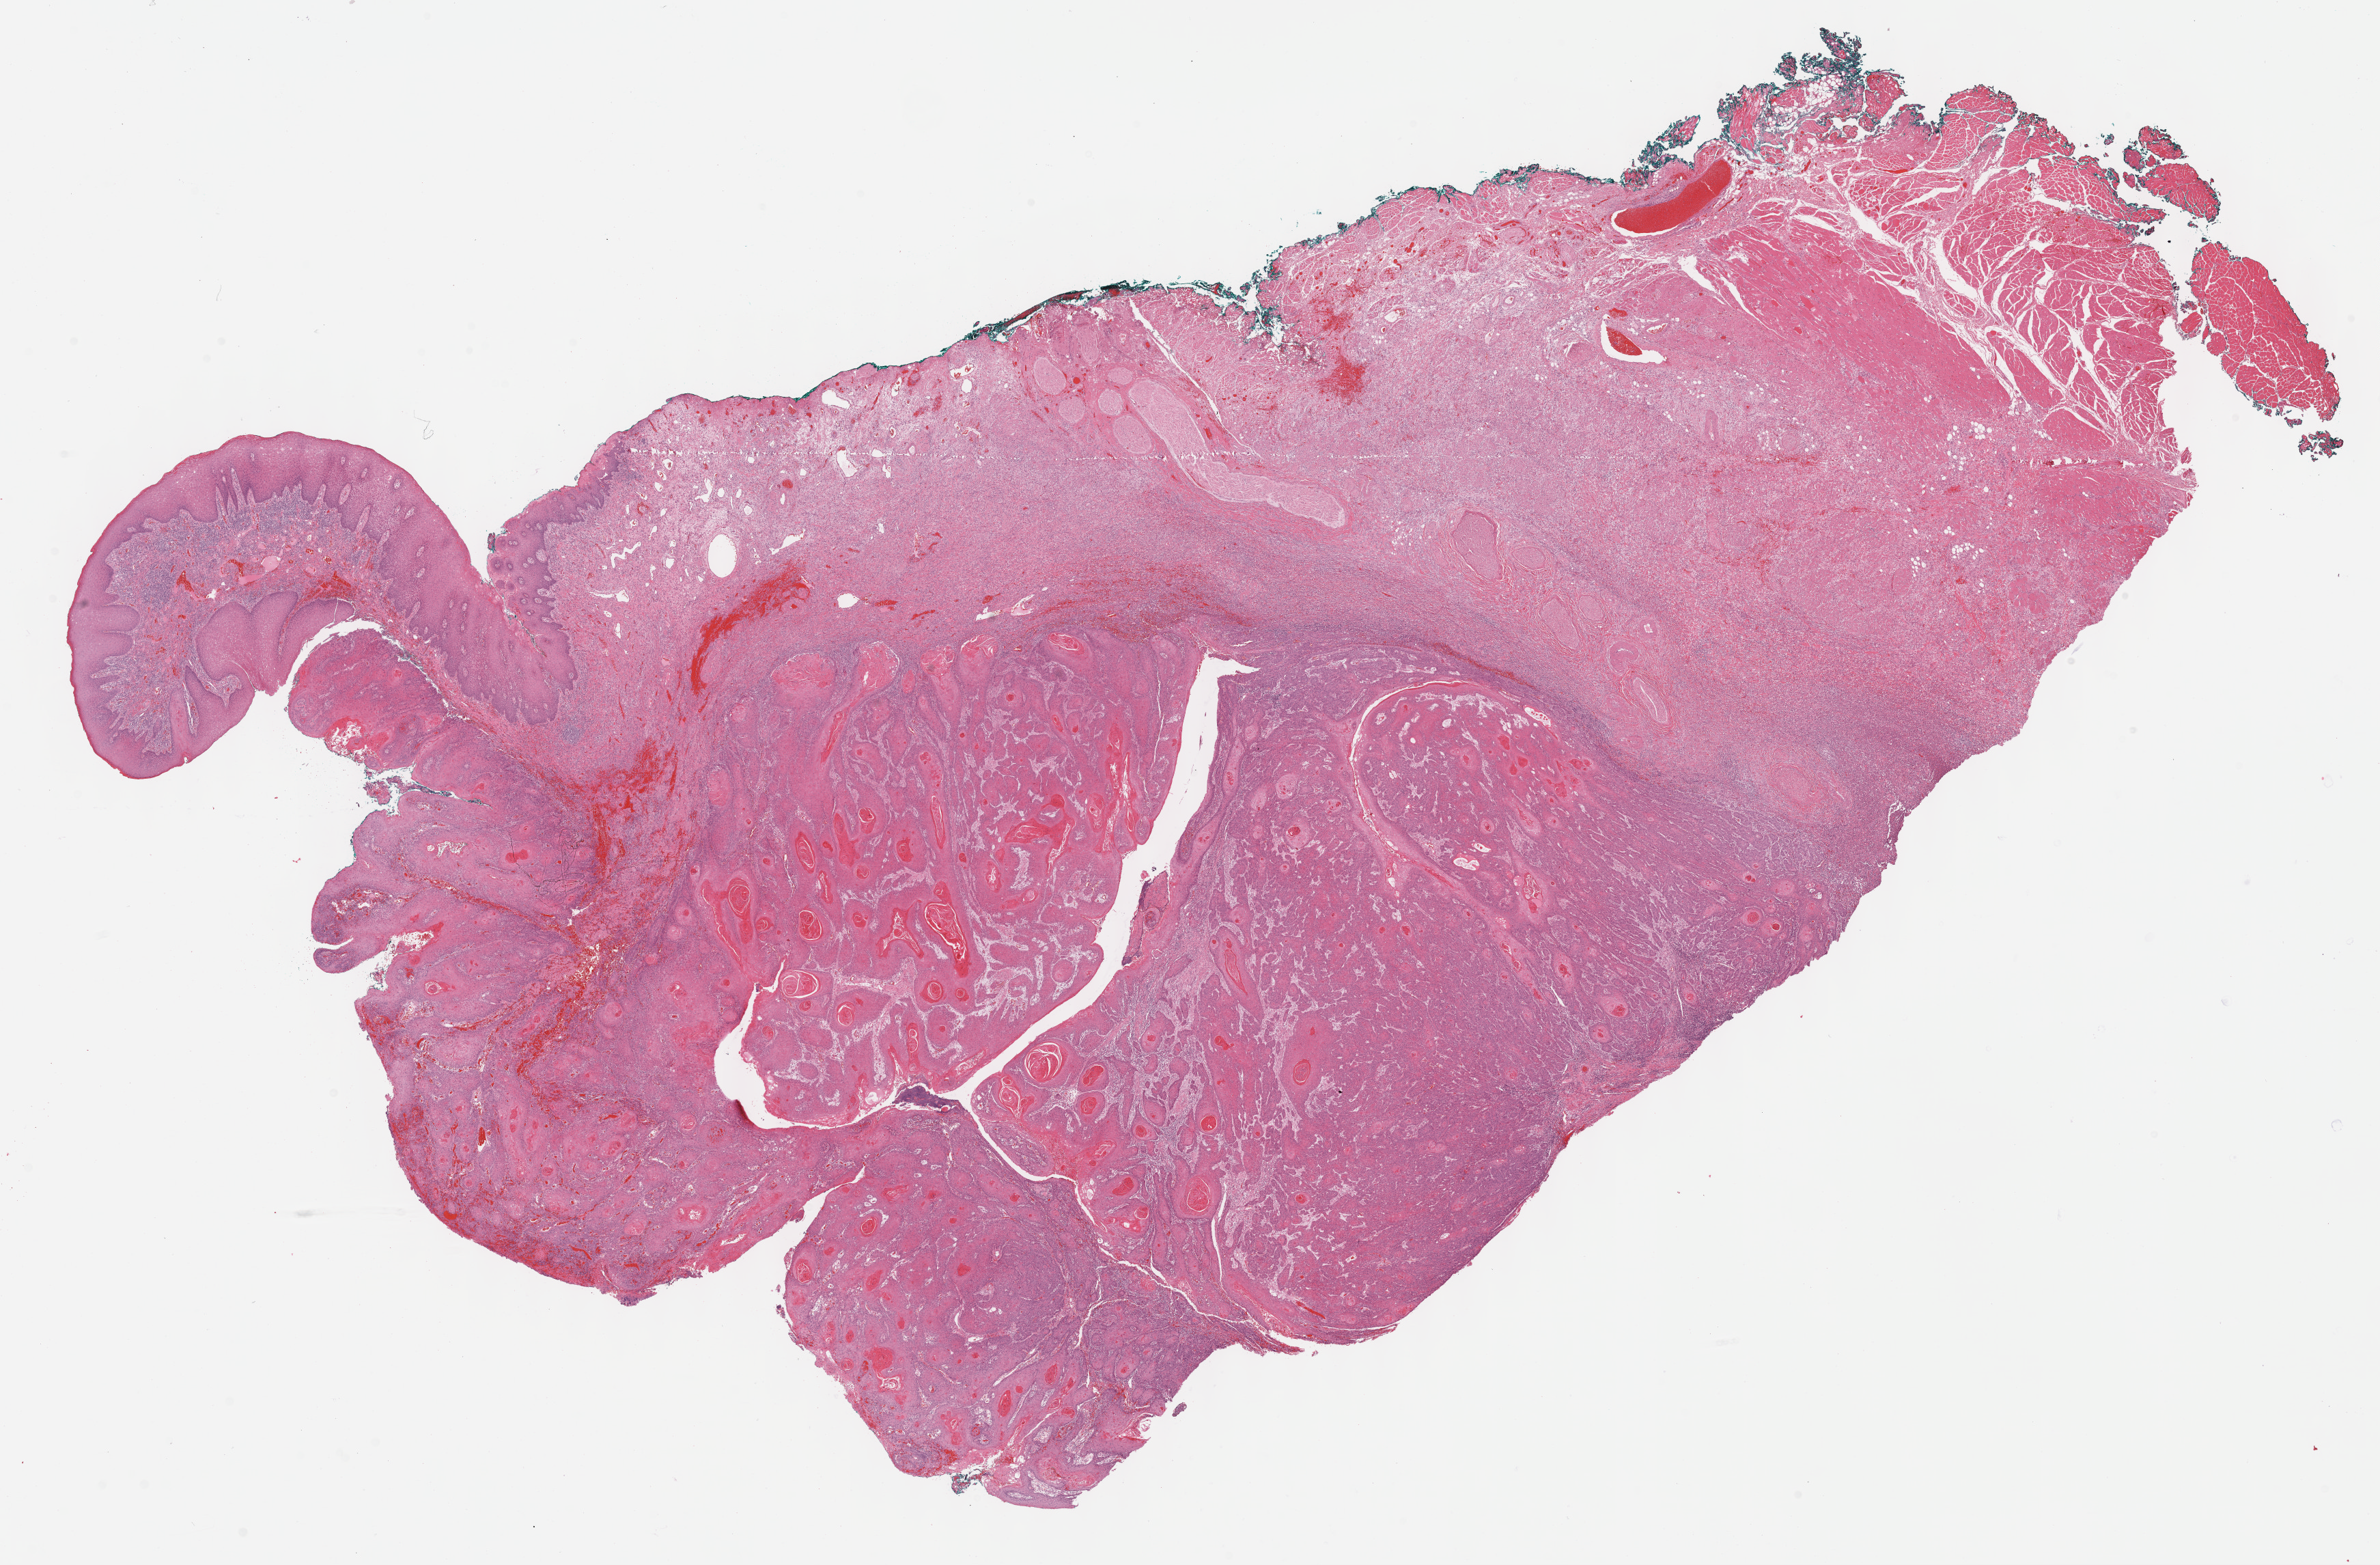
H&E whole-slide image — a low-resolution overview of the entire scanned area, about 28.2 x 18.5 mm (slide scanned at 40x); formalin-fixed paraffin-embedded (FFPE) diagnostic section; primary tumour sample from the head and neck. Patient: male, age at initial diagnosis 82 years. Histologic grade: G1 (well differentiated).
* pathologic diagnosis: Squamous cell carcinoma, keratinizing, NOS (gum, NOS)
* AJCC pathologic stage: III (7th edition)